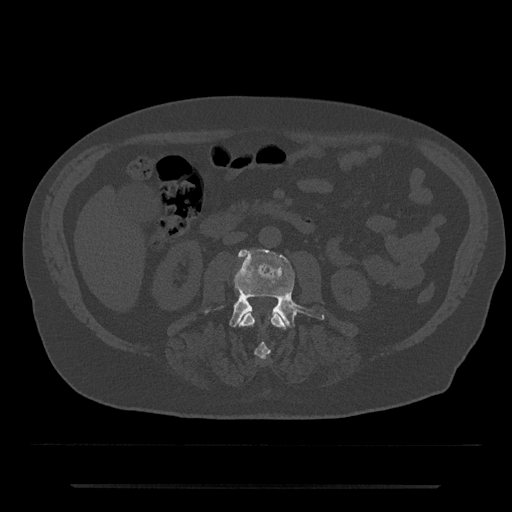
CT including the spine, one axial slice; position 430 of 797 along the scan axis; reconstruction kernel Br40s/3; bone window (W 1800 / L 400 HU); 0.5 mm slice thickness; 512 × 512 image matrix, field of view 434 × 434 mm. Patient: male, 80 years. From the clinical record (not read from this slice): primary cancer: prostate.
Outlined on this slice (semi-automatically segmented with operator editing):
- L2 vertebra: box from (x=239, y=311) to (x=285, y=360) px
- L3 vertebra: (x=205, y=249)–(x=325, y=328)